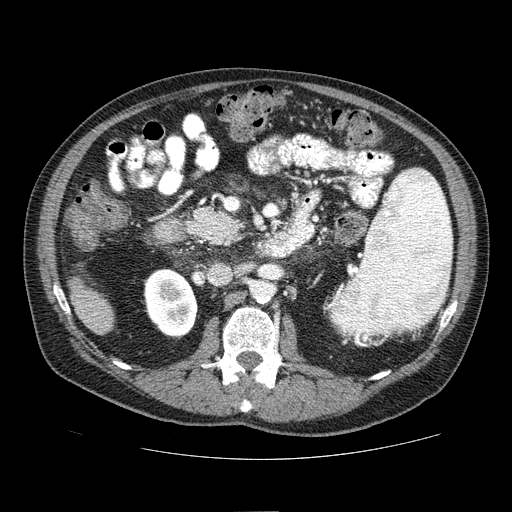
Contrast-enhanced abdominal CT (liver protocol), one axial slice. Slice 20 of 81 in the series (ordered by position). 100 kVp. One of 2 acquisitions stored at this slice position. Soft-tissue window (W 400 / L 40 HU). 2.5 mm slice thickness. 512 × 512 image matrix, field of view 400 × 400 mm. From the clinical record (not read from this slice): diagnosis: hepatocellular carcinoma (patient treated with transarterial chemoembolisation; whether this scan precedes or follows treatment is not stated here); TNM stage (as recorded): Stage-IIIA; Child-Pugh class: A.
Structures marked on this image (semi-automatic segmentation, software-assisted and operator-edited):
- liver parenchyma outside the tumour (the mass and vessels are separate outlines, so this box may not span the whole liver): bounding box [x1, y1, x2, y2] px = [68, 276, 112, 334]
- liver vessels: [95, 313, 98, 315]